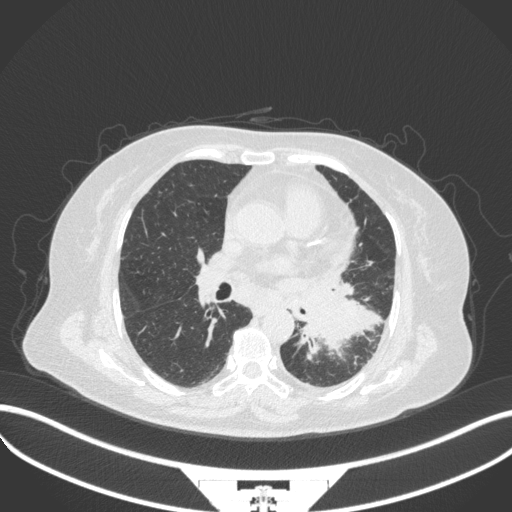
Chest CT, one axial slice. Slice 181 of 328 in the series (ordered by position). 120 kVp. Lung window (W 1500 / L -600 HU). 1 mm slice thickness. 512 × 512 image matrix. Female patient, age 69 years. From the clinical record (not read from this slice): clinical TNM (as recorded): T2b N3 M1.
Structures marked on this image (rectangle marked by the reading radiologist):
- lung tumour (recorded histology: adenocarcinoma): bounding box (x1, y1, x2, y2) in pixels: (303, 289, 384, 363)